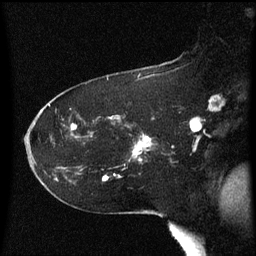
Breast MRI (dynamic contrast-enhanced), one sagittal slice. Slice 38 of 60 in the series (ordered by position). Dynamic contrast-enhanced series, image 2 of 3 at this slice position (ordered by acquisition). 1.5 T. TE 4.2 ms, TR 8.4 ms. 2 mm slice thickness. 256 × 256 image matrix, field of view 200 × 200 mm. Patient: female, 54 years. Case-level facts recorded for this patient, not image findings: setting: breast cancer imaged before/during neoadjuvant chemotherapy; receptor status: HR-positive, HER2-negative.
Structures marked on this image (semi-automatic segmentation, software-assisted and operator-edited):
- analysis volume of interest (the breast-tissue region the enhancement analysis was run in; not a lesion): bounding box <121,122,153,161> (left, top, right, bottom; pixels)
- tumour enhancement mask (voxels above the 70 % enhancement threshold inside the analysis volume of interest): <134,138,153,155>